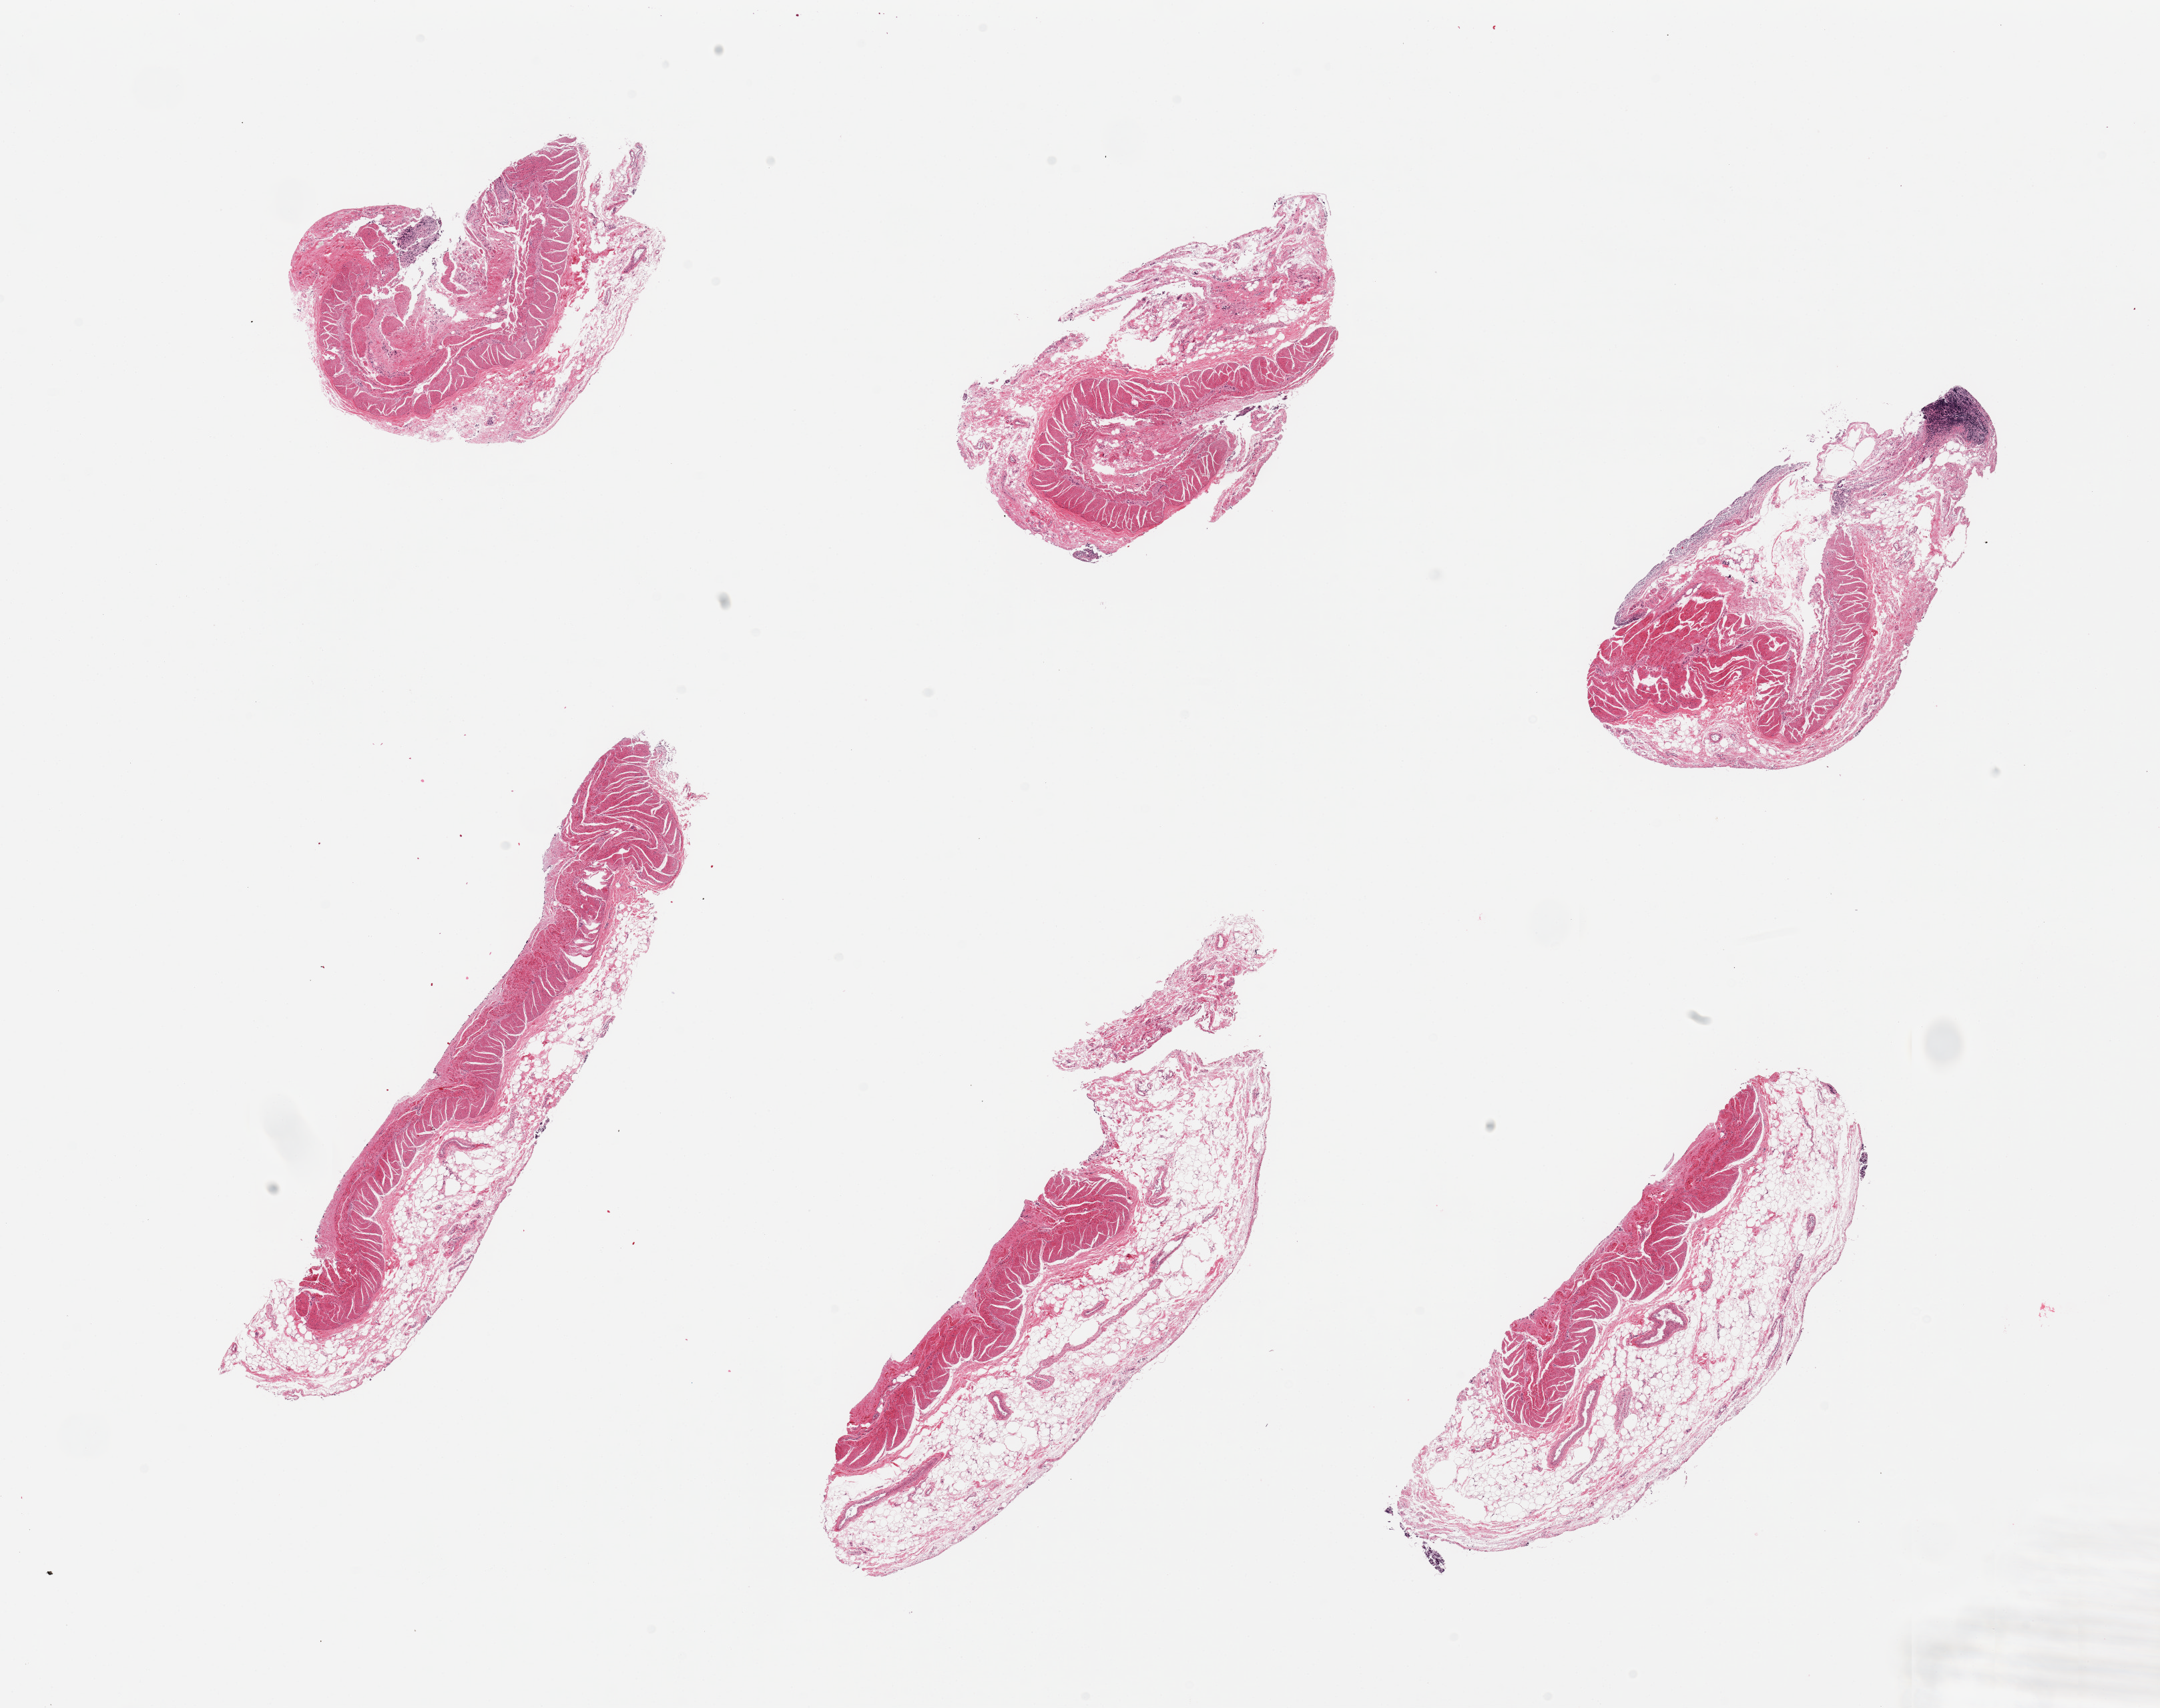
Digitized H&E-stained section — low-resolution overview of the scanned area, about 25.6 x 20.2 mm (from a 20x scan); PAXgene-fixed, paraffin-embedded tissue; target tissue: ileum; donor tissue sample. Donor sex: male.
• reviewer comment on this tissue sample: 6 pieces; predominantly muscularis and fat (not target) with minimal residual autolyzed mucosa and rare lymphoid aggregate